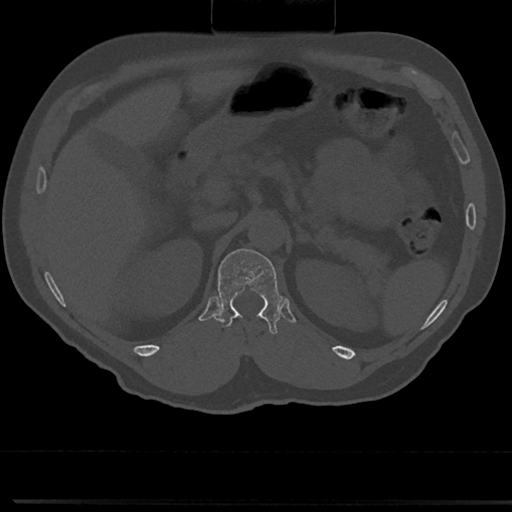
CT including the spine, one axial slice; position 150 of 817 along the scan axis; reconstruction kernel Br40s/3; 120 kVp; bone window (W 1800 / L 400 HU); 512 × 512 image matrix. Male patient, age 61 years. From the clinical record (not read from this slice): primary cancer: prostate.
Structures marked on this image (semi-automatically segmented with operator editing):
- T12 vertebra: box from (x=213, y=245) to (x=279, y=335) px